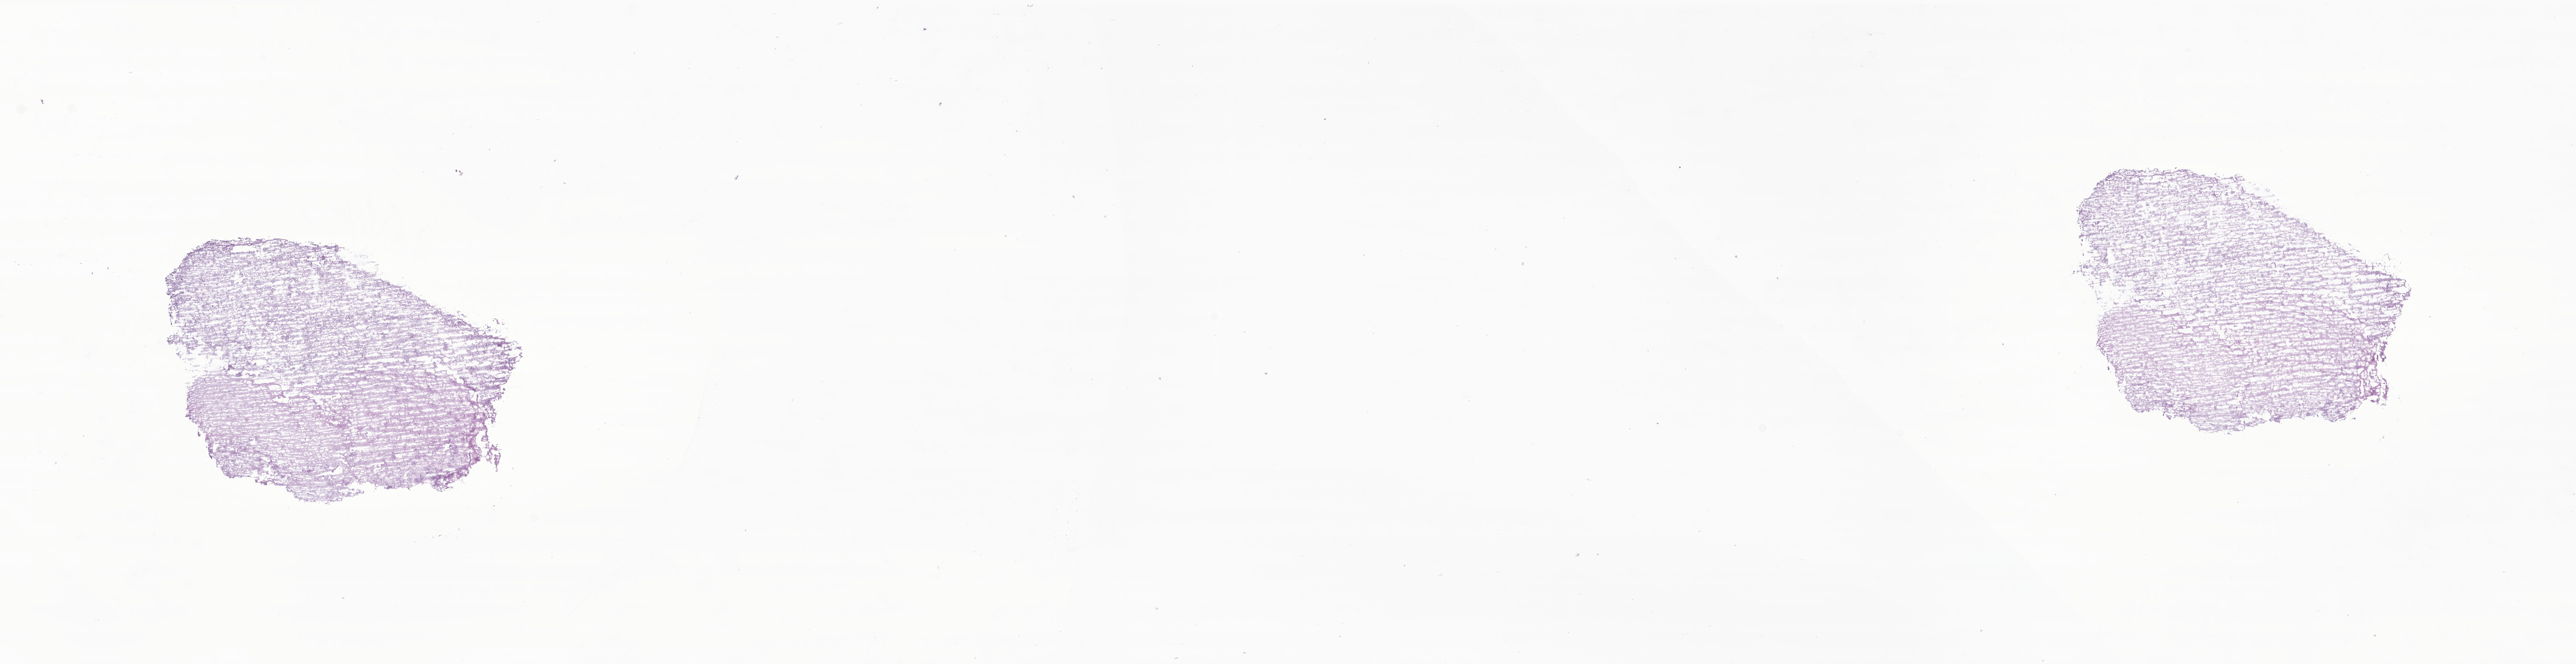
Whole-slide image, H&E stain of tumor tissue from the spinal cord, shown as a low-resolution overview of the whole scanned area (about 28.6 x 7.4 mm), frozen section. Female patient, age 574 days (about 1.6 years).
* diagnosis (ICD-O-3 morphology term): Astrocytoma, NOS